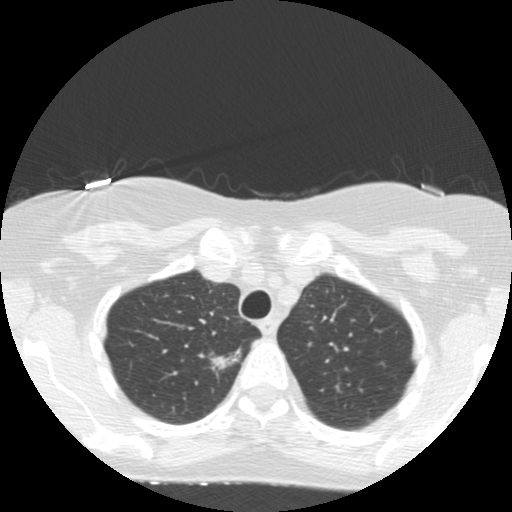
Low-dose screening chest CT, axial slice; baseline annual screen; lung window (W 1500 / L -600 HU); 2.5 mm slice thickness. Female participant, aged 67 years at enrolment. Former smoker at enrolment.
• Expert reader's lesion annotation, bounding box <195,339,254,386> (left, top, right, bottom; pixels).
• Reader record for this screening exam (exam-level; its link to the box is not recorded): non-calcified nodule or mass ≥4 mm, right upper lobe, 16 × 7 mm, poorly defined margins, mixed attenuation.
• Official screen result: positive, change unspecified: nodule(s) >= 4 mm or enlarging nodule(s), mass(es), or other non-specific abnormalities suspicious for lung cancer.
• Lung cancer was diagnosed 132 days after this screen: adenocarcinoma, NOS, right upper lobe, moderately differentiated (G2), stage IA (AJCC 6th edition), 13 mm at pathology.